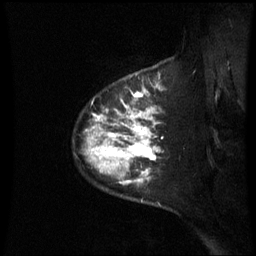
Breast MRI (dynamic contrast-enhanced), one sagittal slice. Slice 50 of 60 in the series (ordered by position). Dynamic contrast-enhanced series, image 2 of 3 at this slice position (ordered by acquisition). 1.5 T. TE 4.2 ms, TR 8.9 ms. 2.4 mm slice thickness. 256 × 256 image matrix. Female patient, age 42 years. Case-level facts recorded for this patient, not image findings: setting: breast cancer imaged before/during neoadjuvant chemotherapy; receptor status: HER2-positive.
Structures marked on this image (semi-automatic segmentation, software-assisted and operator-edited):
- analysis volume of interest (the breast-tissue region the enhancement analysis was run in; not a lesion): bounding box [x1, y1, x2, y2] px = [85, 93, 161, 206]
- tumour enhancement mask (voxels above the 70 % enhancement threshold inside the analysis volume of interest): [86, 93, 158, 185]